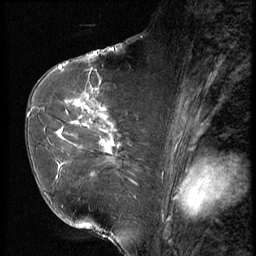
Breast MRI (dynamic contrast-enhanced), one sagittal slice. Slice 37 of 56 in the series (ordered by position). 3 images stored at this slice position (order not interpretable as contrast timing). 1.5 T. TE 4.2 ms, TR 9 ms. 2.5 mm slice thickness. 256 × 256 image matrix, field of view 180 × 180 mm. Female patient, age 61 years. Case-level facts recorded for this patient, not image findings: setting: breast cancer imaged before/during neoadjuvant chemotherapy; receptor status: HR-positive, HER2-negative.
Outlined on this slice (semi-automatic segmentation, software-assisted and operator-edited):
- analysis volume of interest (the breast-tissue region the enhancement analysis was run in; not a lesion): bounding box [x1, y1, x2, y2] px = [47, 89, 153, 191]
- tumour enhancement mask (voxels above the 140 % enhancement threshold inside the analysis volume of interest): [56, 103, 118, 167]